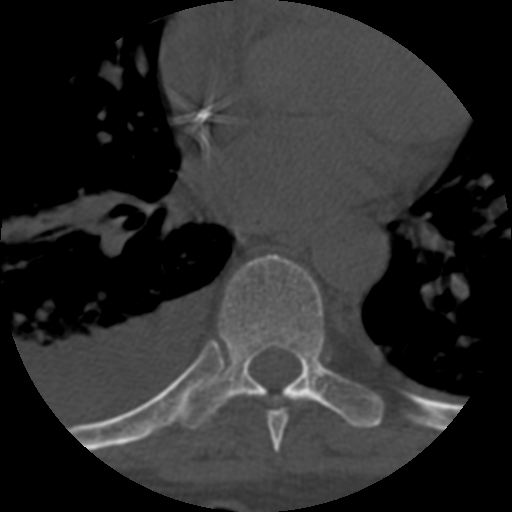
CT including the spine, one axial slice; slice 402 of 708 in the series (ordered by position); reconstruction kernel STANDARD; 120 kVp; one of 3 acquisitions stored at this slice position; bone window (W 1800 / L 400 HU); 512 × 512 image matrix, field of view 160 × 160 mm. Patient age 55 years. From the clinical record (not read from this slice): primary cancer: colon; vertebrae with lytic lesions (as recorded): T12, L1, L5.
Structures marked on this image (semi-automatic segmentation, software-assisted and operator-edited):
- T7 vertebra: bounding box [x1, y1, x2, y2] px = [266, 409, 288, 452]
- T8 vertebra: [180, 255, 383, 429]